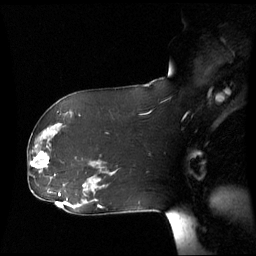
Breast MRI (dynamic contrast-enhanced), one sagittal slice. Position 35 of 60 along the scan axis. Dynamic contrast-enhanced series, image 2 of 3 at this slice position (ordered by acquisition). 1.5 T. TE 4.2 ms, TR 8.9 ms. 2.7 mm slice thickness. 256 × 256 image matrix, field of view 280 × 280 mm. Patient: female, 61 years. Case-level facts recorded for this patient, not image findings: setting: breast cancer imaged before/during neoadjuvant chemotherapy; receptor status: HR-positive, HER2-negative.
Outlined on this slice (semi-automatically segmented with operator editing):
- analysis volume of interest (the breast-tissue region the enhancement analysis was run in; not a lesion): bounding box <28,142,55,177> (left, top, right, bottom; pixels)
- tumour enhancement mask (voxels above the 70 % enhancement threshold inside the analysis volume of interest): <32,152,49,169>